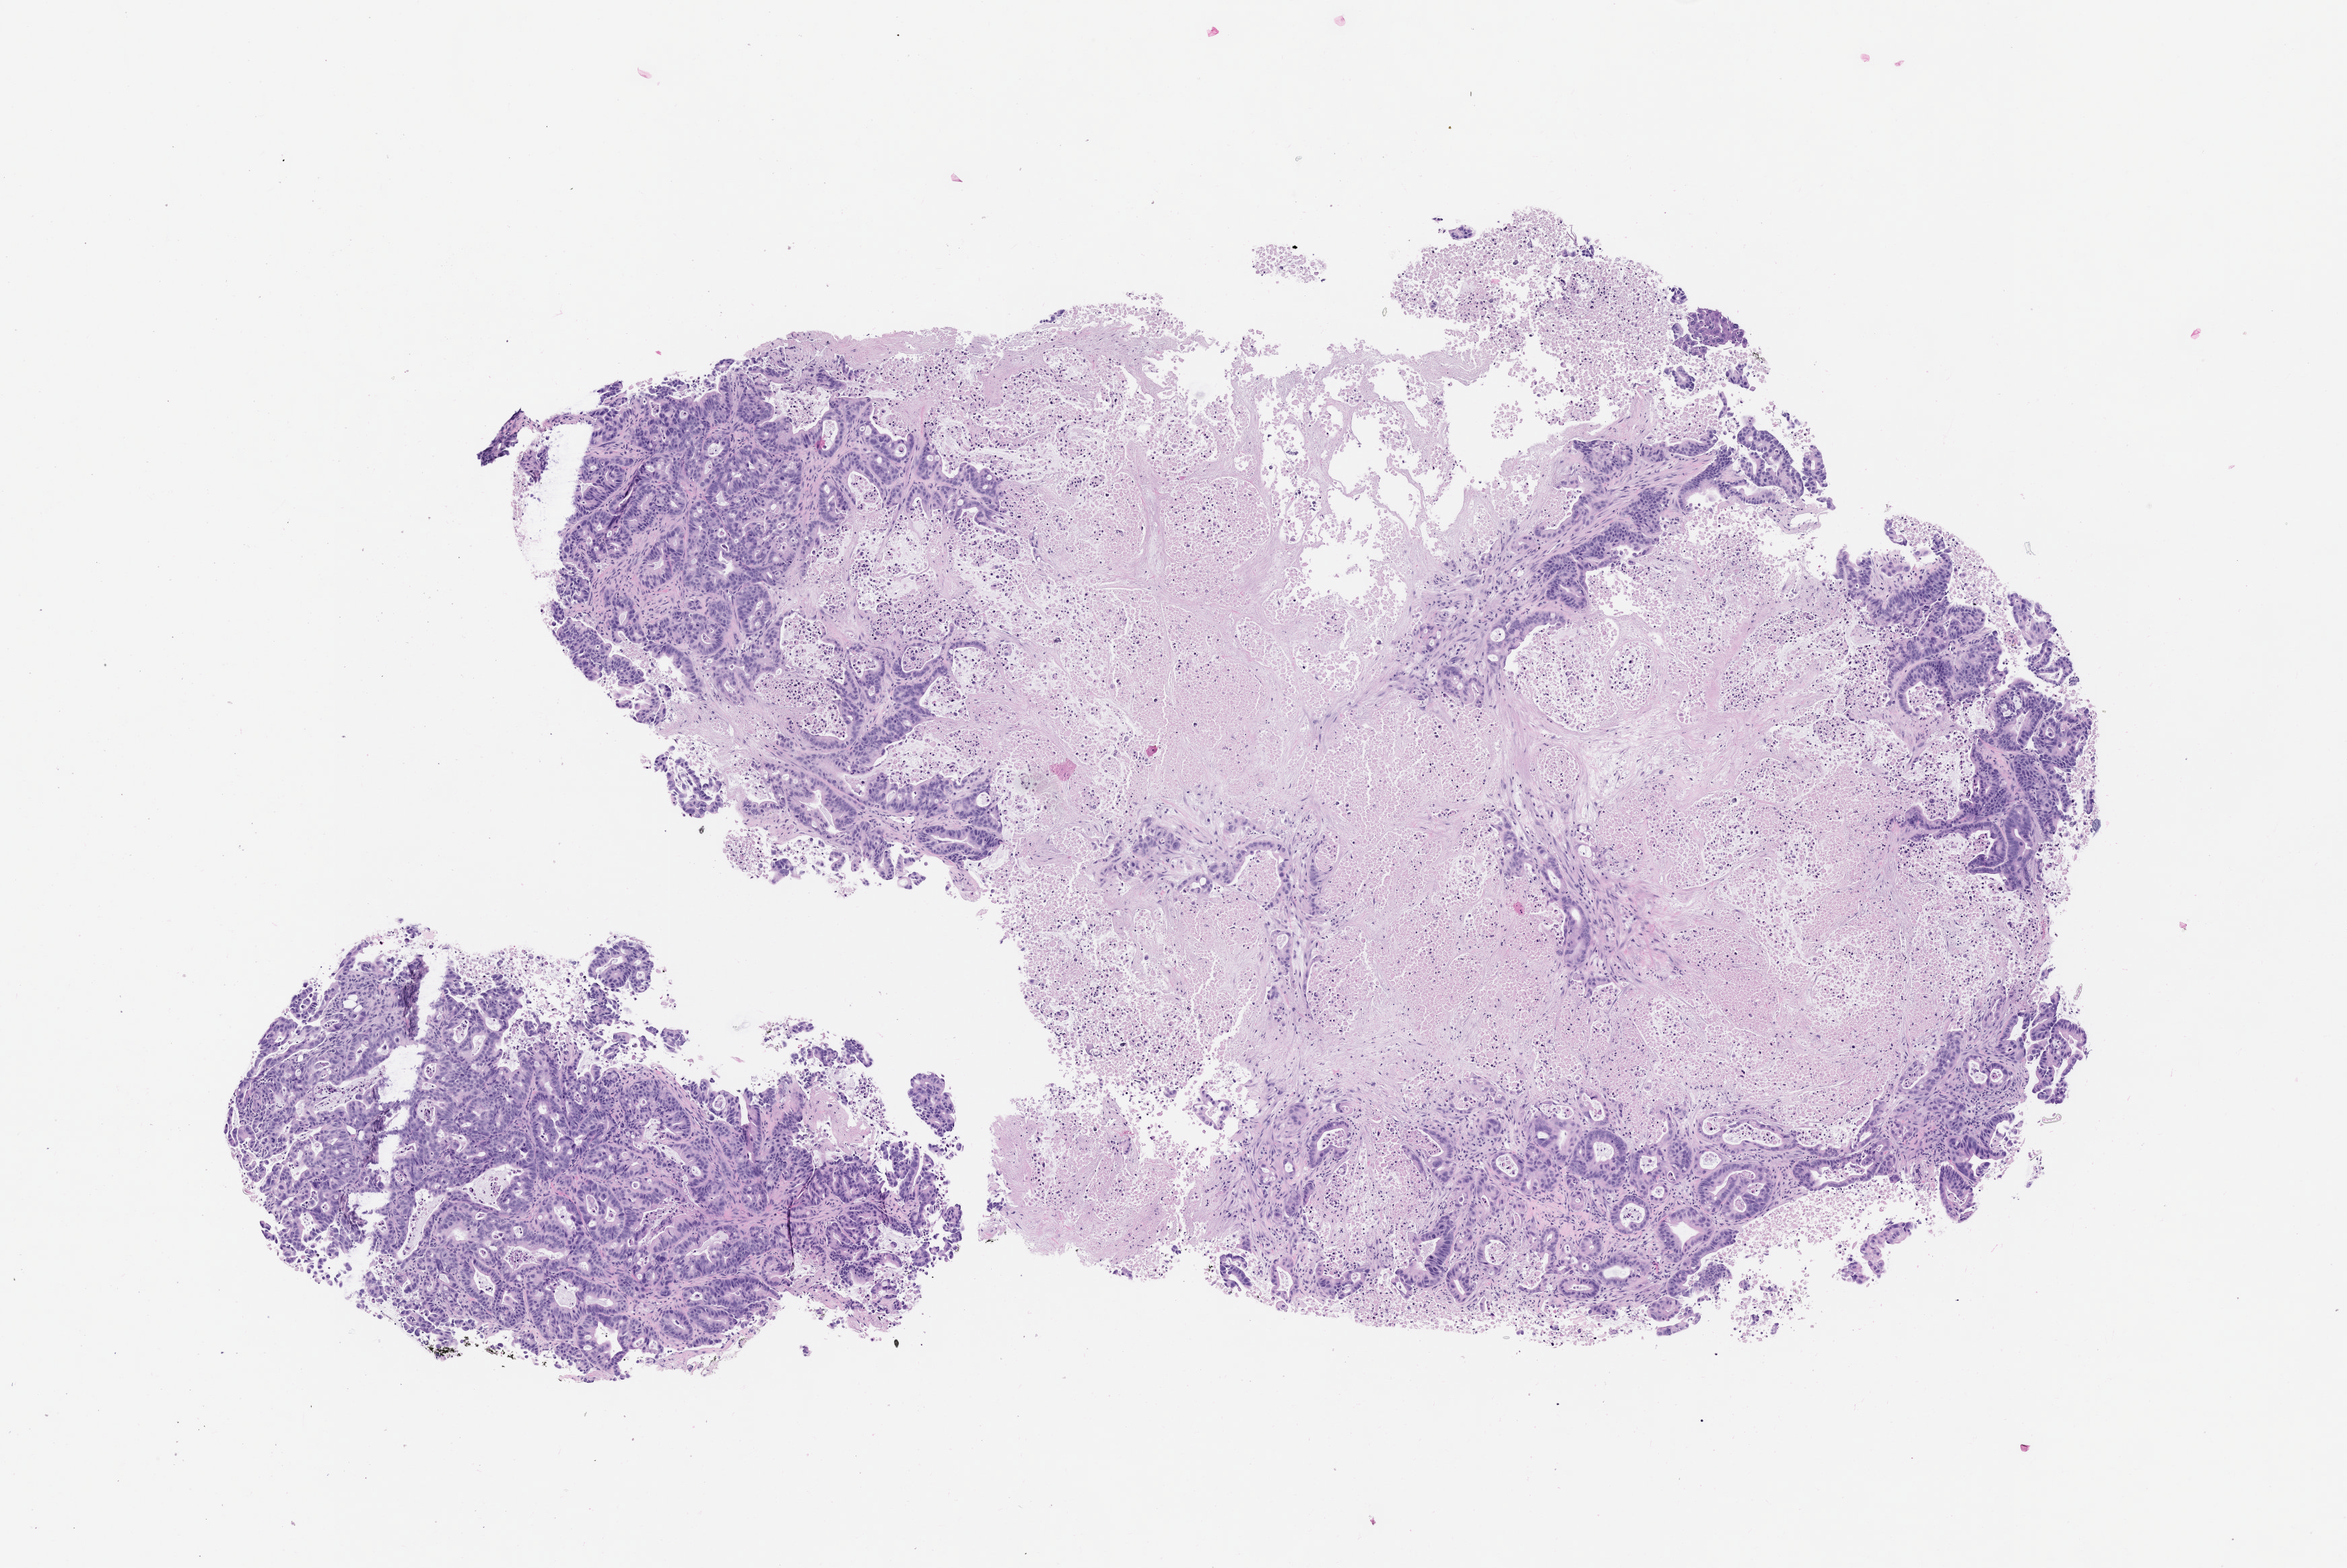
Hematoxylin and eosin (H&E) whole-slide image of a patient-derived xenograft (PDX) tumor grown in a mouse, passage 2 — whole scanned area (about 7.0 x 4.7 mm) shown as a low-resolution overview; FFPE section; originating tumor site category: pancreas.
* originating patient diagnosis: Pancreatic Adenocarcinoma